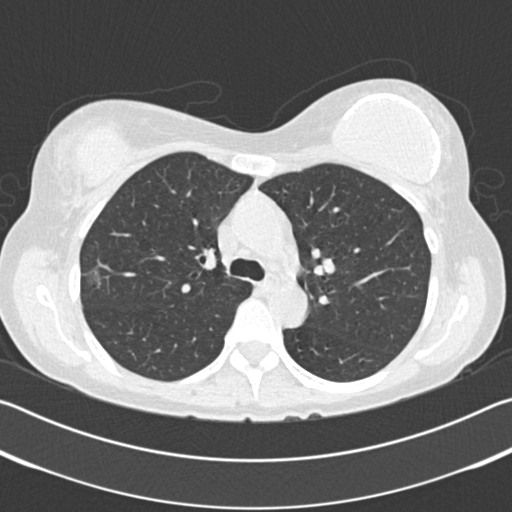
Low-dose screening chest CT, axial slice; second annual screen; lung window (W 1500 / L -600 HU); 2 mm slice thickness; standard (soft-tissue) reconstruction kernel (B30f); 512 × 512 image matrix, field of view 340 × 340 mm. Female participant, aged 58 years at enrolment. Former smoker at enrolment.
Expert-annotated lung lesion, bounding box [x1, y1, x2, y2] px = [68, 256, 120, 309]. The exam's reader record, not a measurement of the box and not confirmed to be the same lesion: non-calcified nodule or mass ≥4 mm, right upper lobe, 15 × 13 mm, poorly defined margins, ground glass attenuation, pre-existing on the prior screen: no. Later outcome: lung cancer diagnosed 120 days after this screen — bronchiolo-alveolar adenocarcinoma, NOS, right upper lobe, well differentiated (G1), stage IA (AJCC 6th edition).